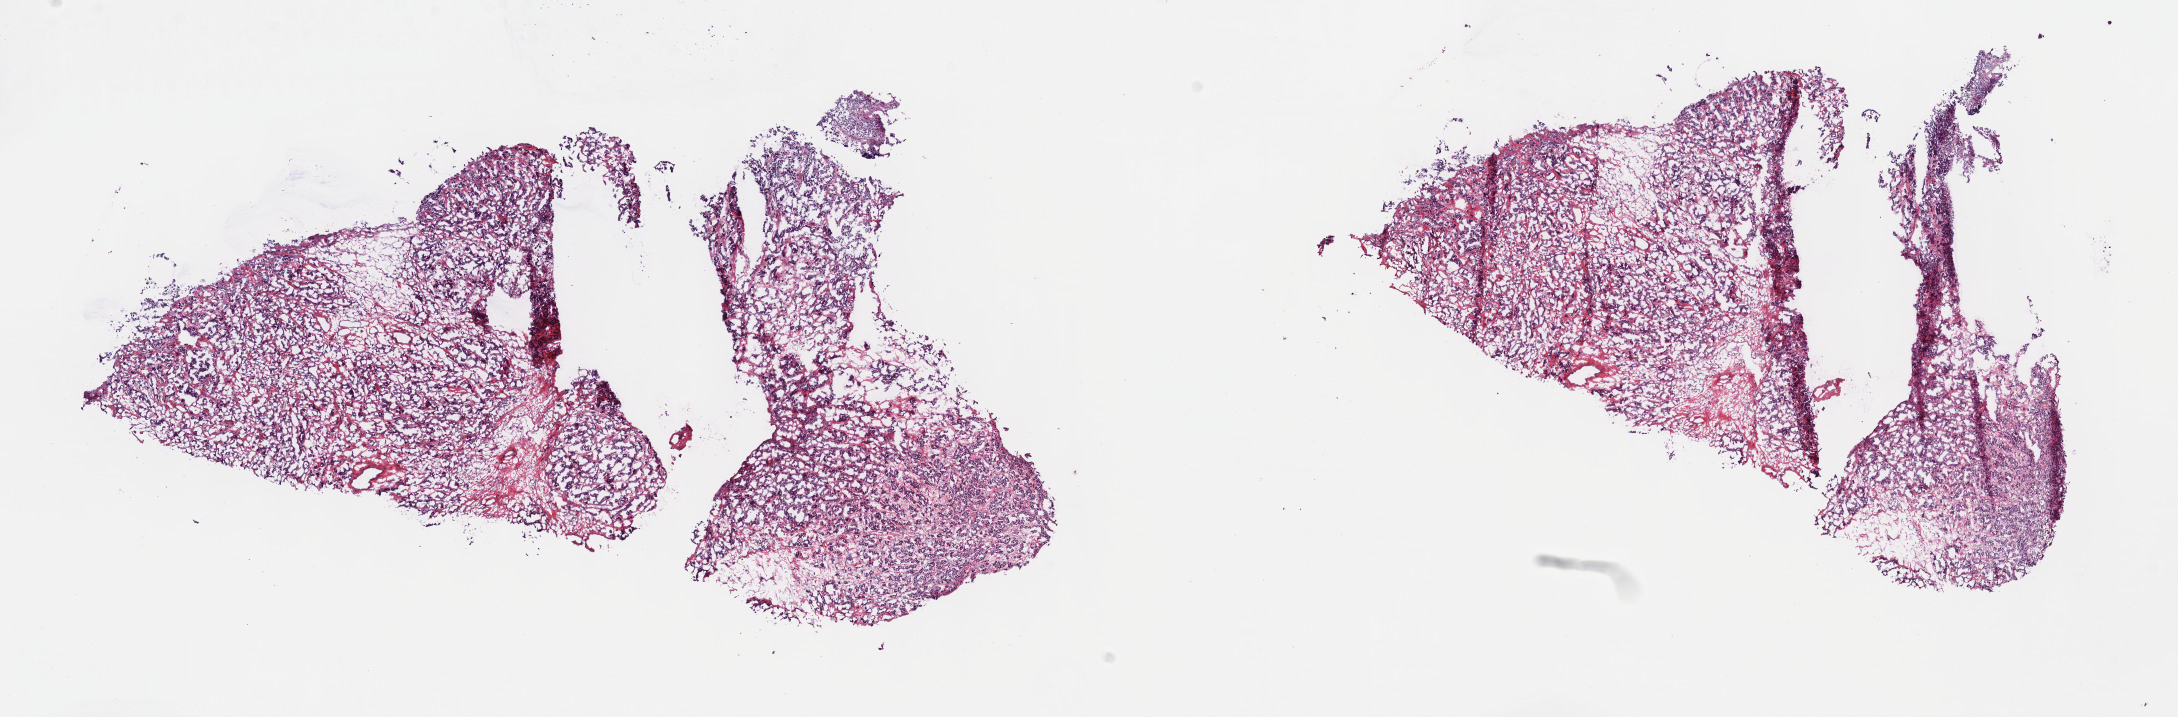
Digitized H&E tissue section (whole slide), whole scanned area (about 17.6 x 5.8 mm) shown as a low-resolution overview, frozen section from the top of the tissue portion, primary tumour sample from the mesothelium. Male patient; age at initial diagnosis 54 years.
Diagnosis: Epithelioid mesothelioma, malignant (pleura, NOS).